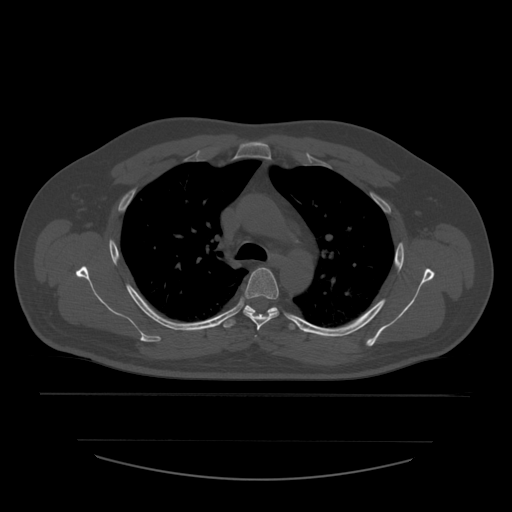
CT including the spine, one axial slice. Bone window (W 1800 / L 400 HU). 512 × 512 image matrix, field of view 441 × 441 mm. Patient age 44 years. From the clinical record (not read from this slice): primary cancer: soft tissue sarcoma.
Outlined on this slice (semi-automatically segmented with operator editing):
- T4 vertebra: bounding box <243,268,280,331> (left, top, right, bottom; pixels)
- T5 vertebra: <223,305,295,330>